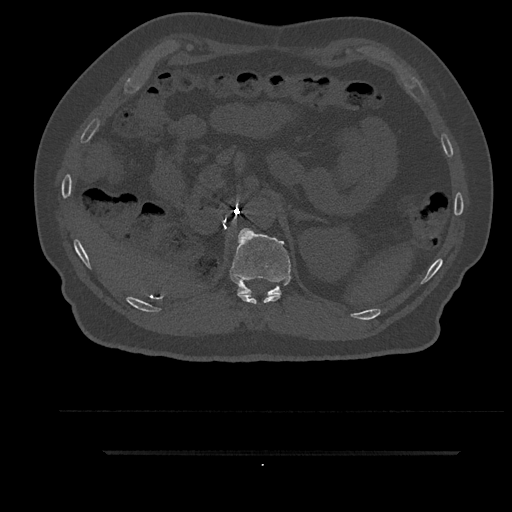
CT including the spine, one axial slice. Slice 267 of 797 in the series (ordered by position). 120 kVp. Bone window (W 1800 / L 400 HU). 0.5 mm slice thickness. 512 × 512 image matrix. Patient: male, 63 years. From the clinical record (not read from this slice): primary cancer: renal.
Structures marked on this image (semi-automatic segmentation, software-assisted and operator-edited):
- T11 vertebra: bounding box <238,293,281,304> (left, top, right, bottom; pixels)
- T12 vertebra: <230,228,291,296>